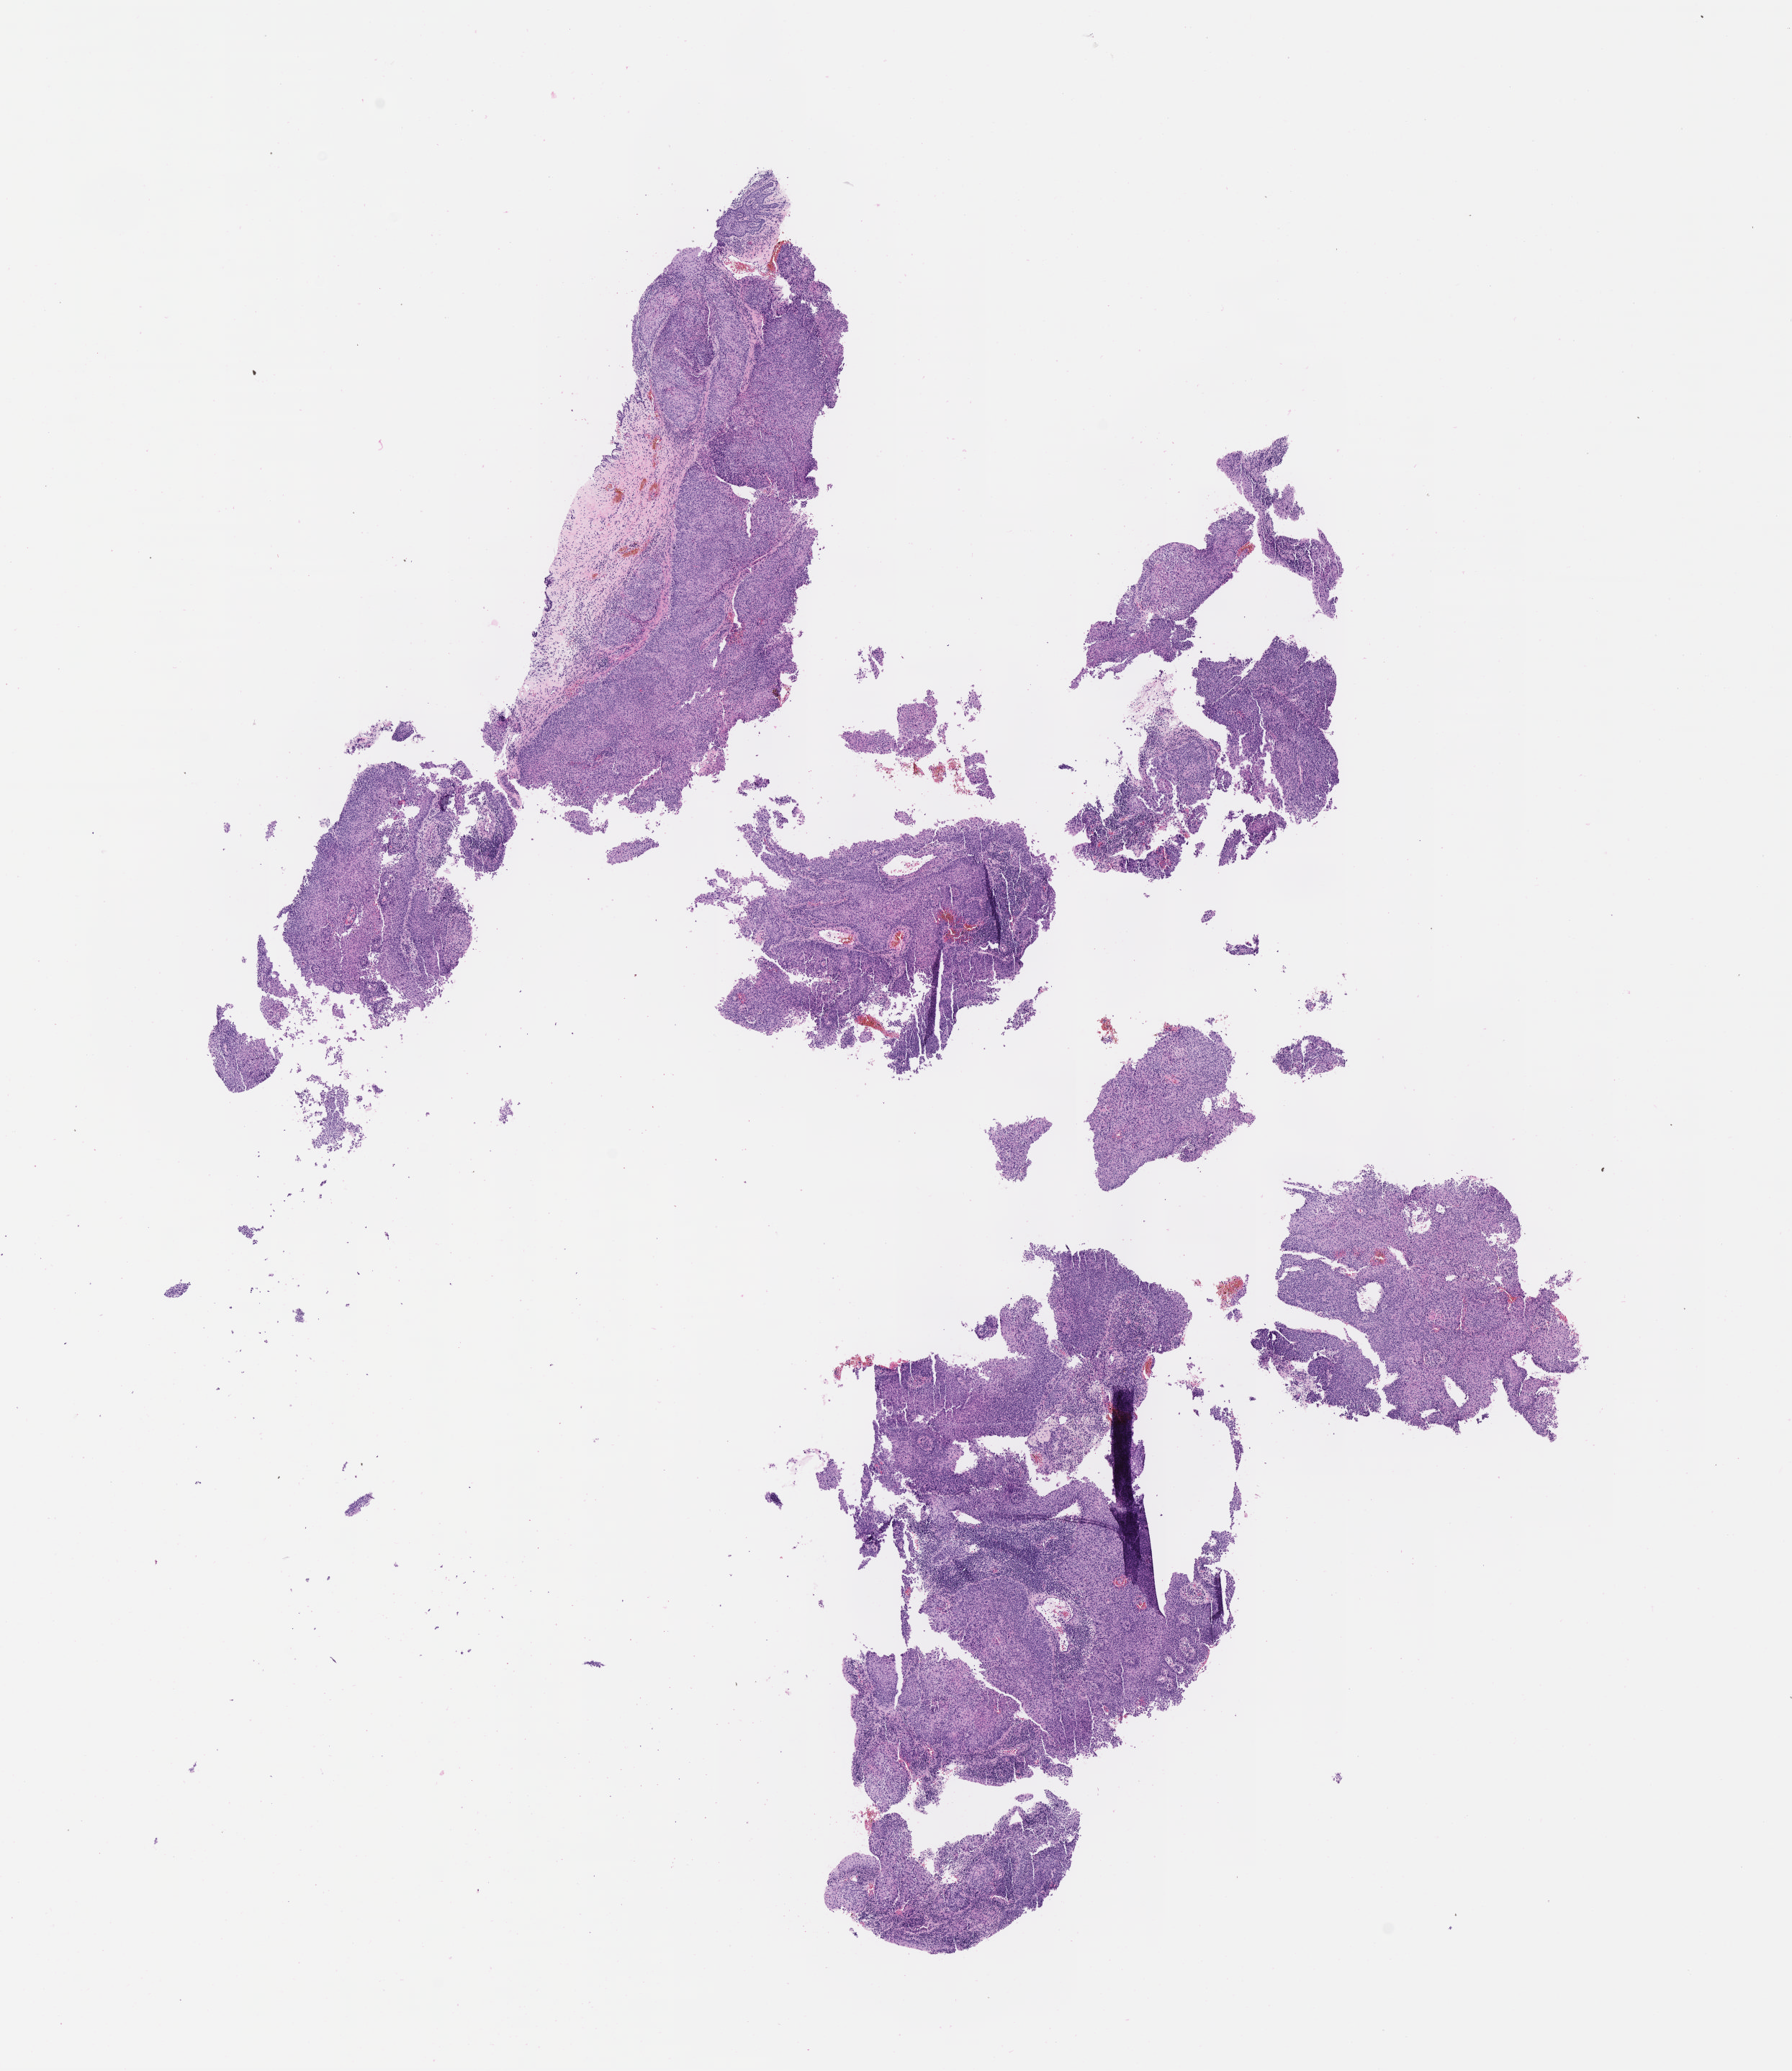
Digitized hematoxylin and eosin (H&E)-stained section, shown as a low-resolution overview of the whole scanned area (about 10.1 x 11.6 mm); specimen: tumor tissue; site: cervix. Patient female; 40 years old.
* histologic diagnosis: Squamous cell carcinoma, large cell, nonkeratinizing, NOS